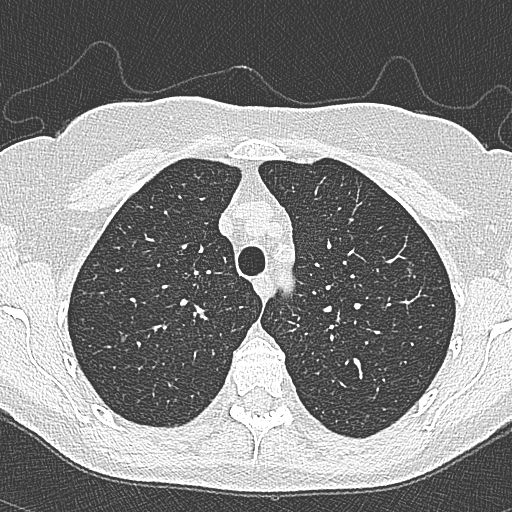
Axial slice from a low-dose chest CT screening exam, second annual screen, lung window (W 1500 / L -600 HU), 1 mm slice thickness, slice 75 of 350 in the series. Female participant, aged 65 years at enrolment. Current smoker at enrolment.
- Expert-annotated lung lesion, bounding box [x1, y1, x2, y2] px = [392, 250, 432, 292].
- The screening reader recorded 4 non-calcified nodules or masses ≥4 mm on this exam (left upper lobe, left upper lobe, left upper lobe, right lower lobe); which of them this box marks is not recorded.
- Official screen result: positive, change unspecified: nodule(s) >= 4 mm or enlarging nodule(s), mass(es), or other non-specific abnormalities suspicious for lung cancer.
- Lung cancer was diagnosed 54 days after this screen: bronchiolo-alveolar carcinoma, non-mucinous, left upper lobe, stage IA (AJCC 6th edition), 10 mm at pathology.